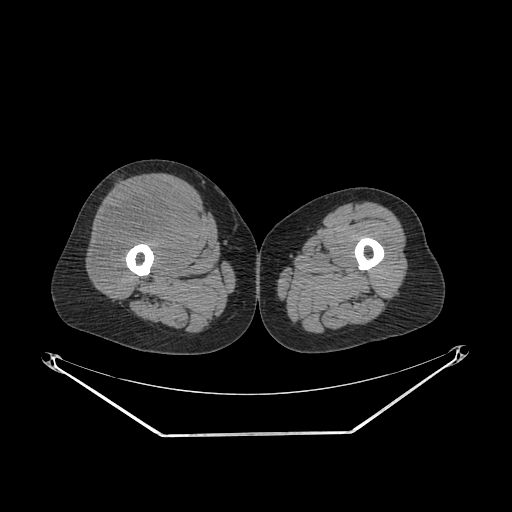
CT of an extremity soft-tissue mass (from a PET/CT study), one axial slice; reconstruction kernel SOFT; 140 kVp; soft-tissue window (W 400 / L 40 HU); 3.75 mm slice thickness; 512 × 512 image matrix, field of view 500 × 500 mm. Female patient. Case-level facts recorded for this patient, not image findings: histological type: pleiomorphic undifferentiated sarcoma; grade: high; site of the primary tumour: right quadricep.
Annotated regions visible in this slice (expert contour drawn on MRI and transferred to this co-registered scan by the dataset authors):
- tumour plus oedema (research contour): bounding box <96,189,195,282> (left, top, right, bottom; pixels)
- tumour (research contour): <96,189,195,282>